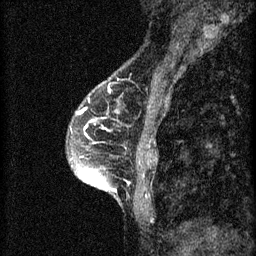
Breast MRI (dynamic contrast-enhanced), one sagittal slice. Position 20 of 60 along the scan axis. 3 images stored at this slice position (order not interpretable as contrast timing). 1.5 T. TE 4.2 ms, TR 8.2 ms. 256 × 256 image matrix. Patient: female, 45 years.
Annotated regions visible in this slice (semi-automatic segmentation, software-assisted and operator-edited):
- analysis volume of interest (the breast-tissue region the enhancement analysis was run in; not a lesion): bounding box [x1, y1, x2, y2] px = [68, 104, 157, 217]
- tumour enhancement mask (voxels above the 70 % enhancement threshold inside the analysis volume of interest): [78, 110, 117, 191]